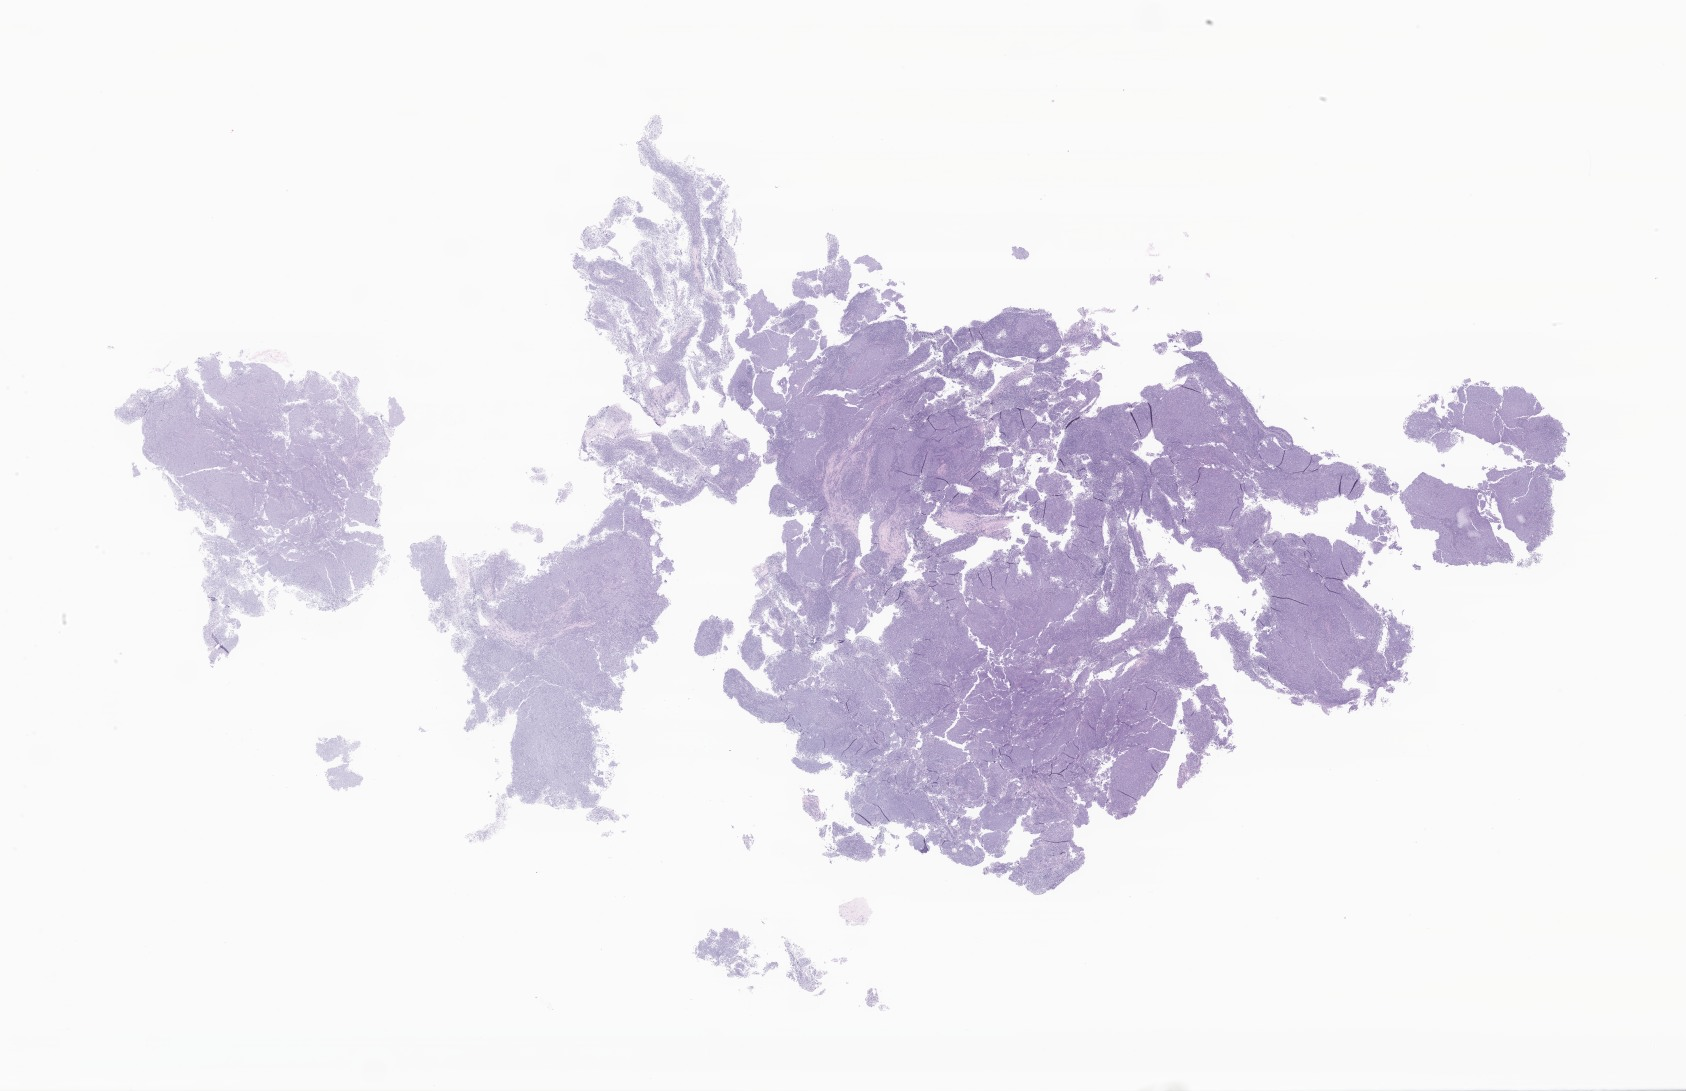
Digitized hematoxylin and eosin (H&E)-stained section of tumor tissue from the nasal cavity, whole scanned area (about 28.4 x 18.4 mm) shown as a low-resolution overview. FFPE section. Patient male; age 187 months.
* diagnosis (ICD-O-3 morphology term): Neoplasm, malignant